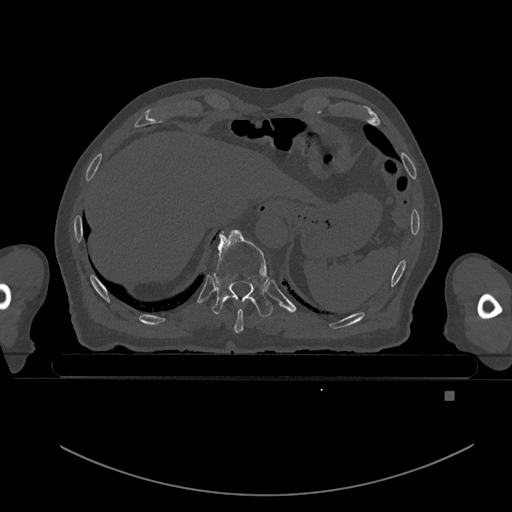
CT including the spine, one axial slice. Position 105 of 969 along the scan axis. Bone window (W 1800 / L 400 HU). 0.5 mm slice thickness. 512 × 512 image matrix, field of view 456 × 456 mm. Male patient, age 82 years. From the clinical record (not read from this slice): primary cancer: prostate.
Annotated regions visible in this slice (semi-automatic segmentation, software-assisted and operator-edited):
- T10 vertebra: bounding box (x1, y1, x2, y2) in pixels: (212, 229, 273, 317)
- T9 vertebra: (234, 309, 243, 333)